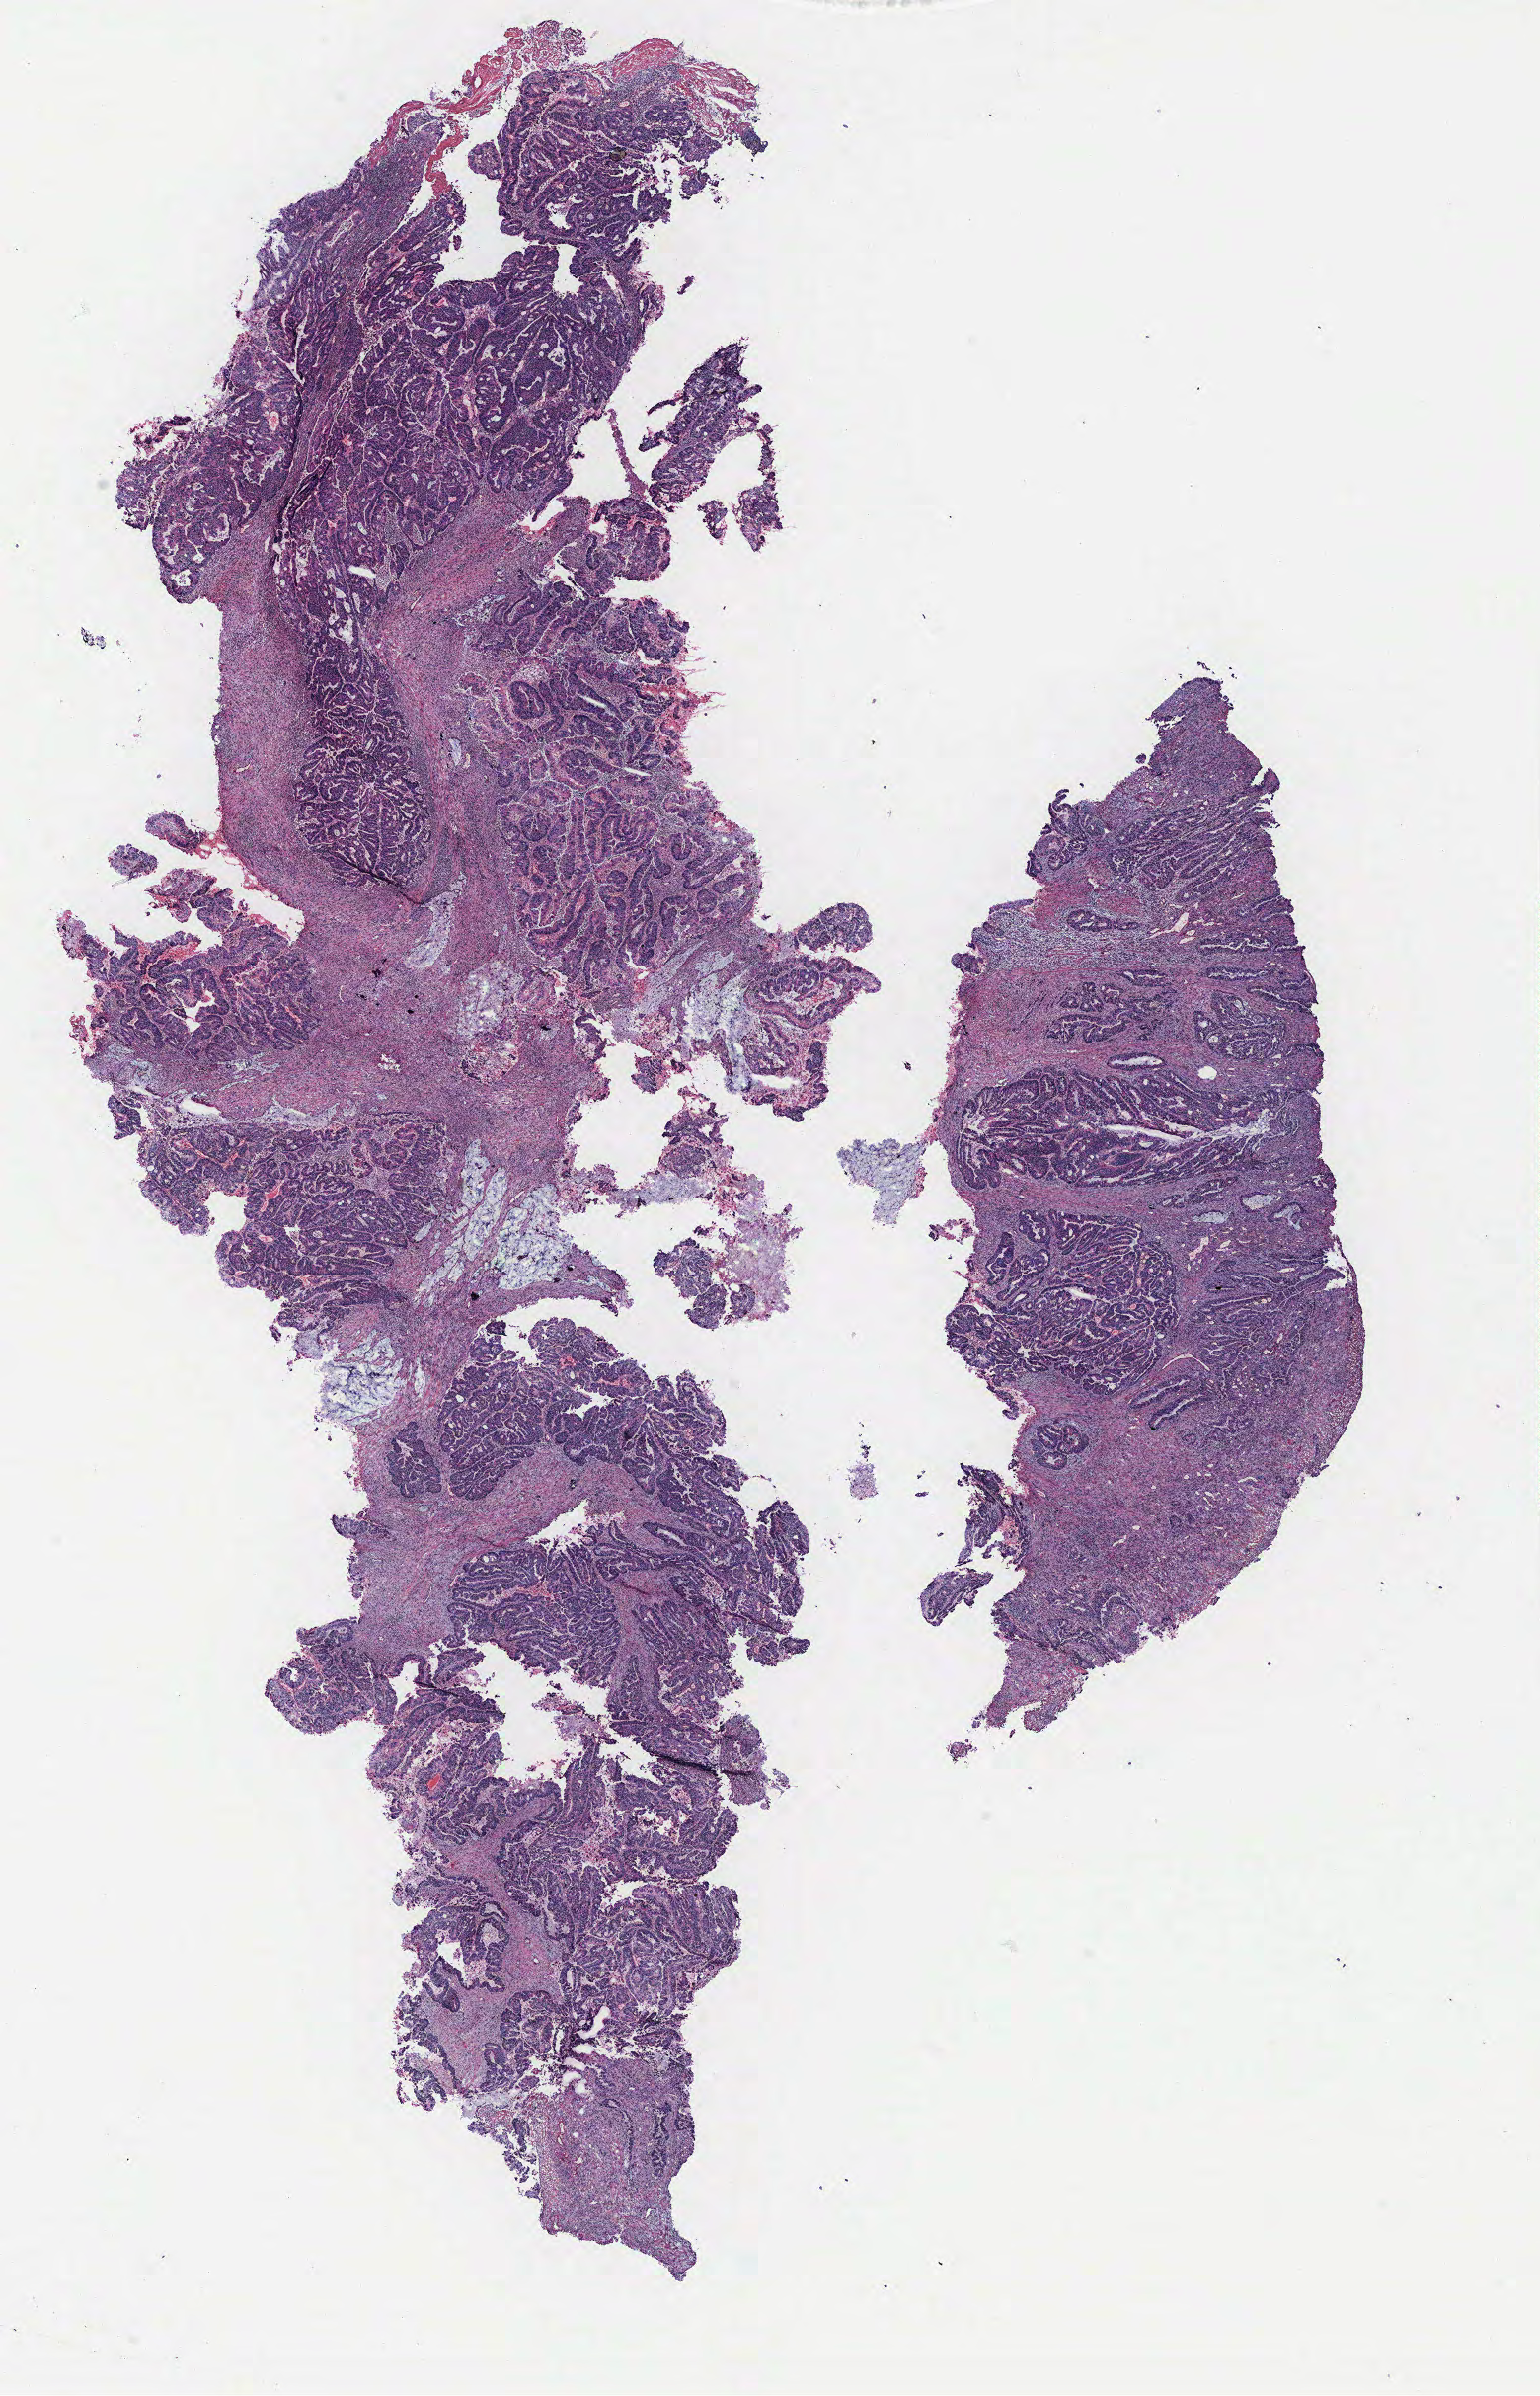
Whole-slide histology image, H&E, low-resolution overview of the scanned area, about 12.5 x 19.4 mm (from a 40x scan). Colon, normal (non-tumour) tissue. 53-year-old male patient.
• this section: normal (non-tumour) tissue from the same patient
• patient diagnosis: Adenocarcinoma, NOS